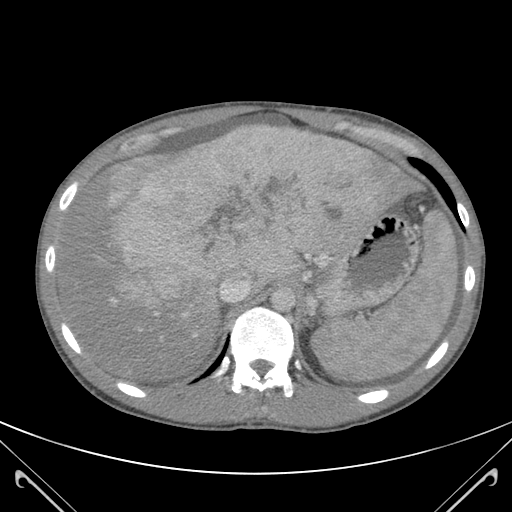
Contrast-enhanced abdominal CT (liver protocol), one axial slice. Position 89 of 118 along the scan axis. 120 kVp. Soft-tissue window (W 400 / L 40 HU). 512 × 512 image matrix, field of view 380 × 380 mm. Case-level facts recorded for this patient, not image findings: diagnosis: hepatocellular carcinoma (patient treated with transarterial chemoembolisation; whether this scan precedes or follows treatment is not stated here); TNM stage (as recorded): Stage-IIIB; Child-Pugh class: A; tumour nodularity: uninodular.
Annotated regions visible in this slice (semi-automatically segmented with operator editing):
- abdominal aorta: bounding box [x1, y1, x2, y2] px = [273, 286, 298, 311]
- liver parenchyma outside the tumour (the mass and vessels are separate outlines, so this box may not span the whole liver): [61, 124, 422, 378]
- mass: [98, 127, 415, 324]
- liver vessels: [111, 273, 251, 337]